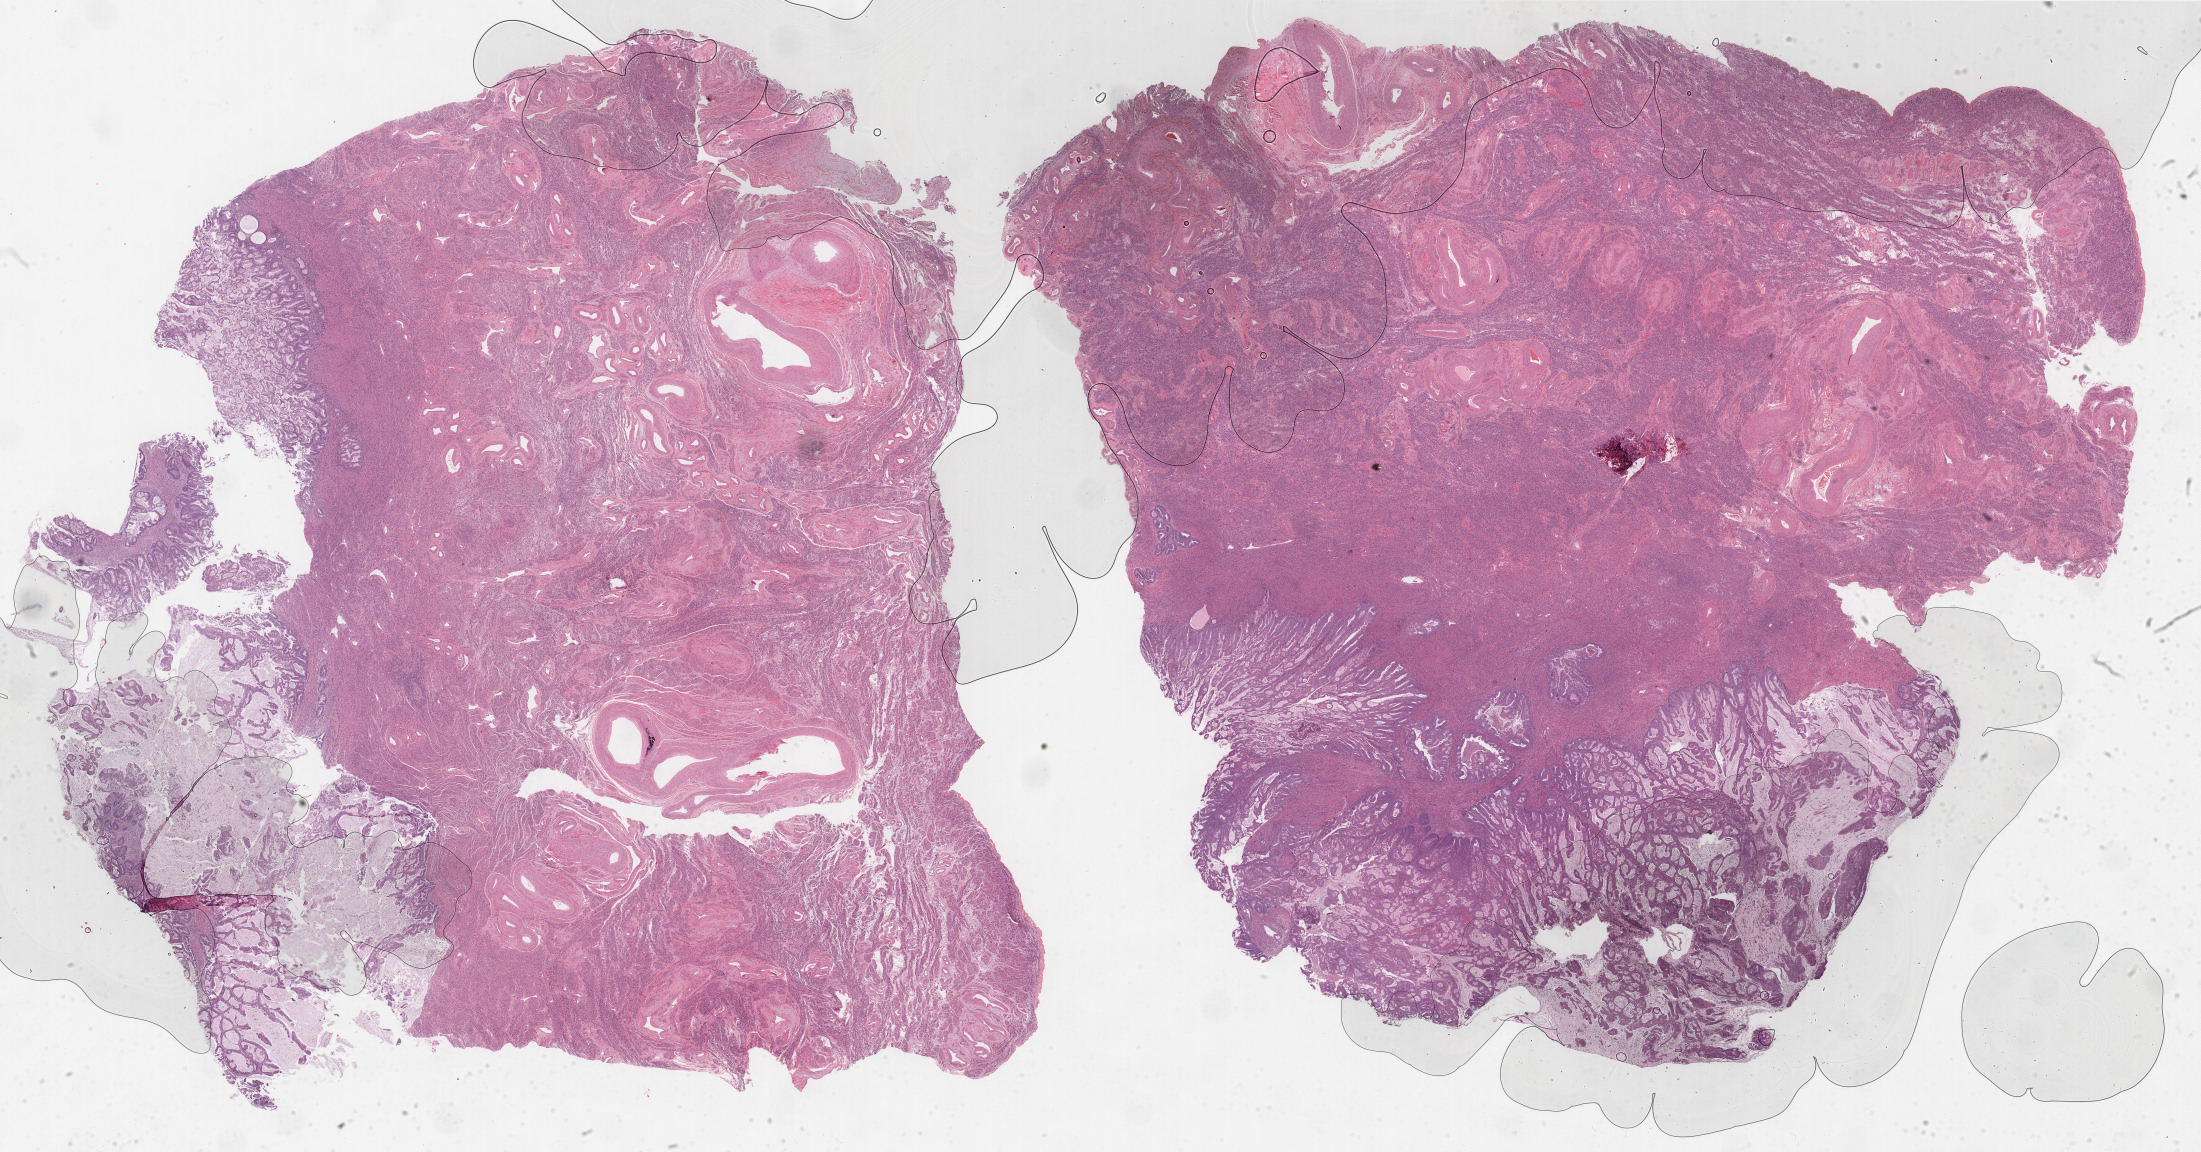
H&E whole-slide image — low-resolution overview of the scanned area, about 34.9 x 18.3 mm (slide scanned at 40x), formalin-fixed paraffin-embedded (FFPE) diagnostic section, sample: primary tumour, uterus. Patient: female, age at initial diagnosis 73 years. Histologic grade: G1 (well differentiated).
Pathologic diagnosis: Endometrioid adenocarcinoma, NOS (endometrium). FIGO stage: IB.